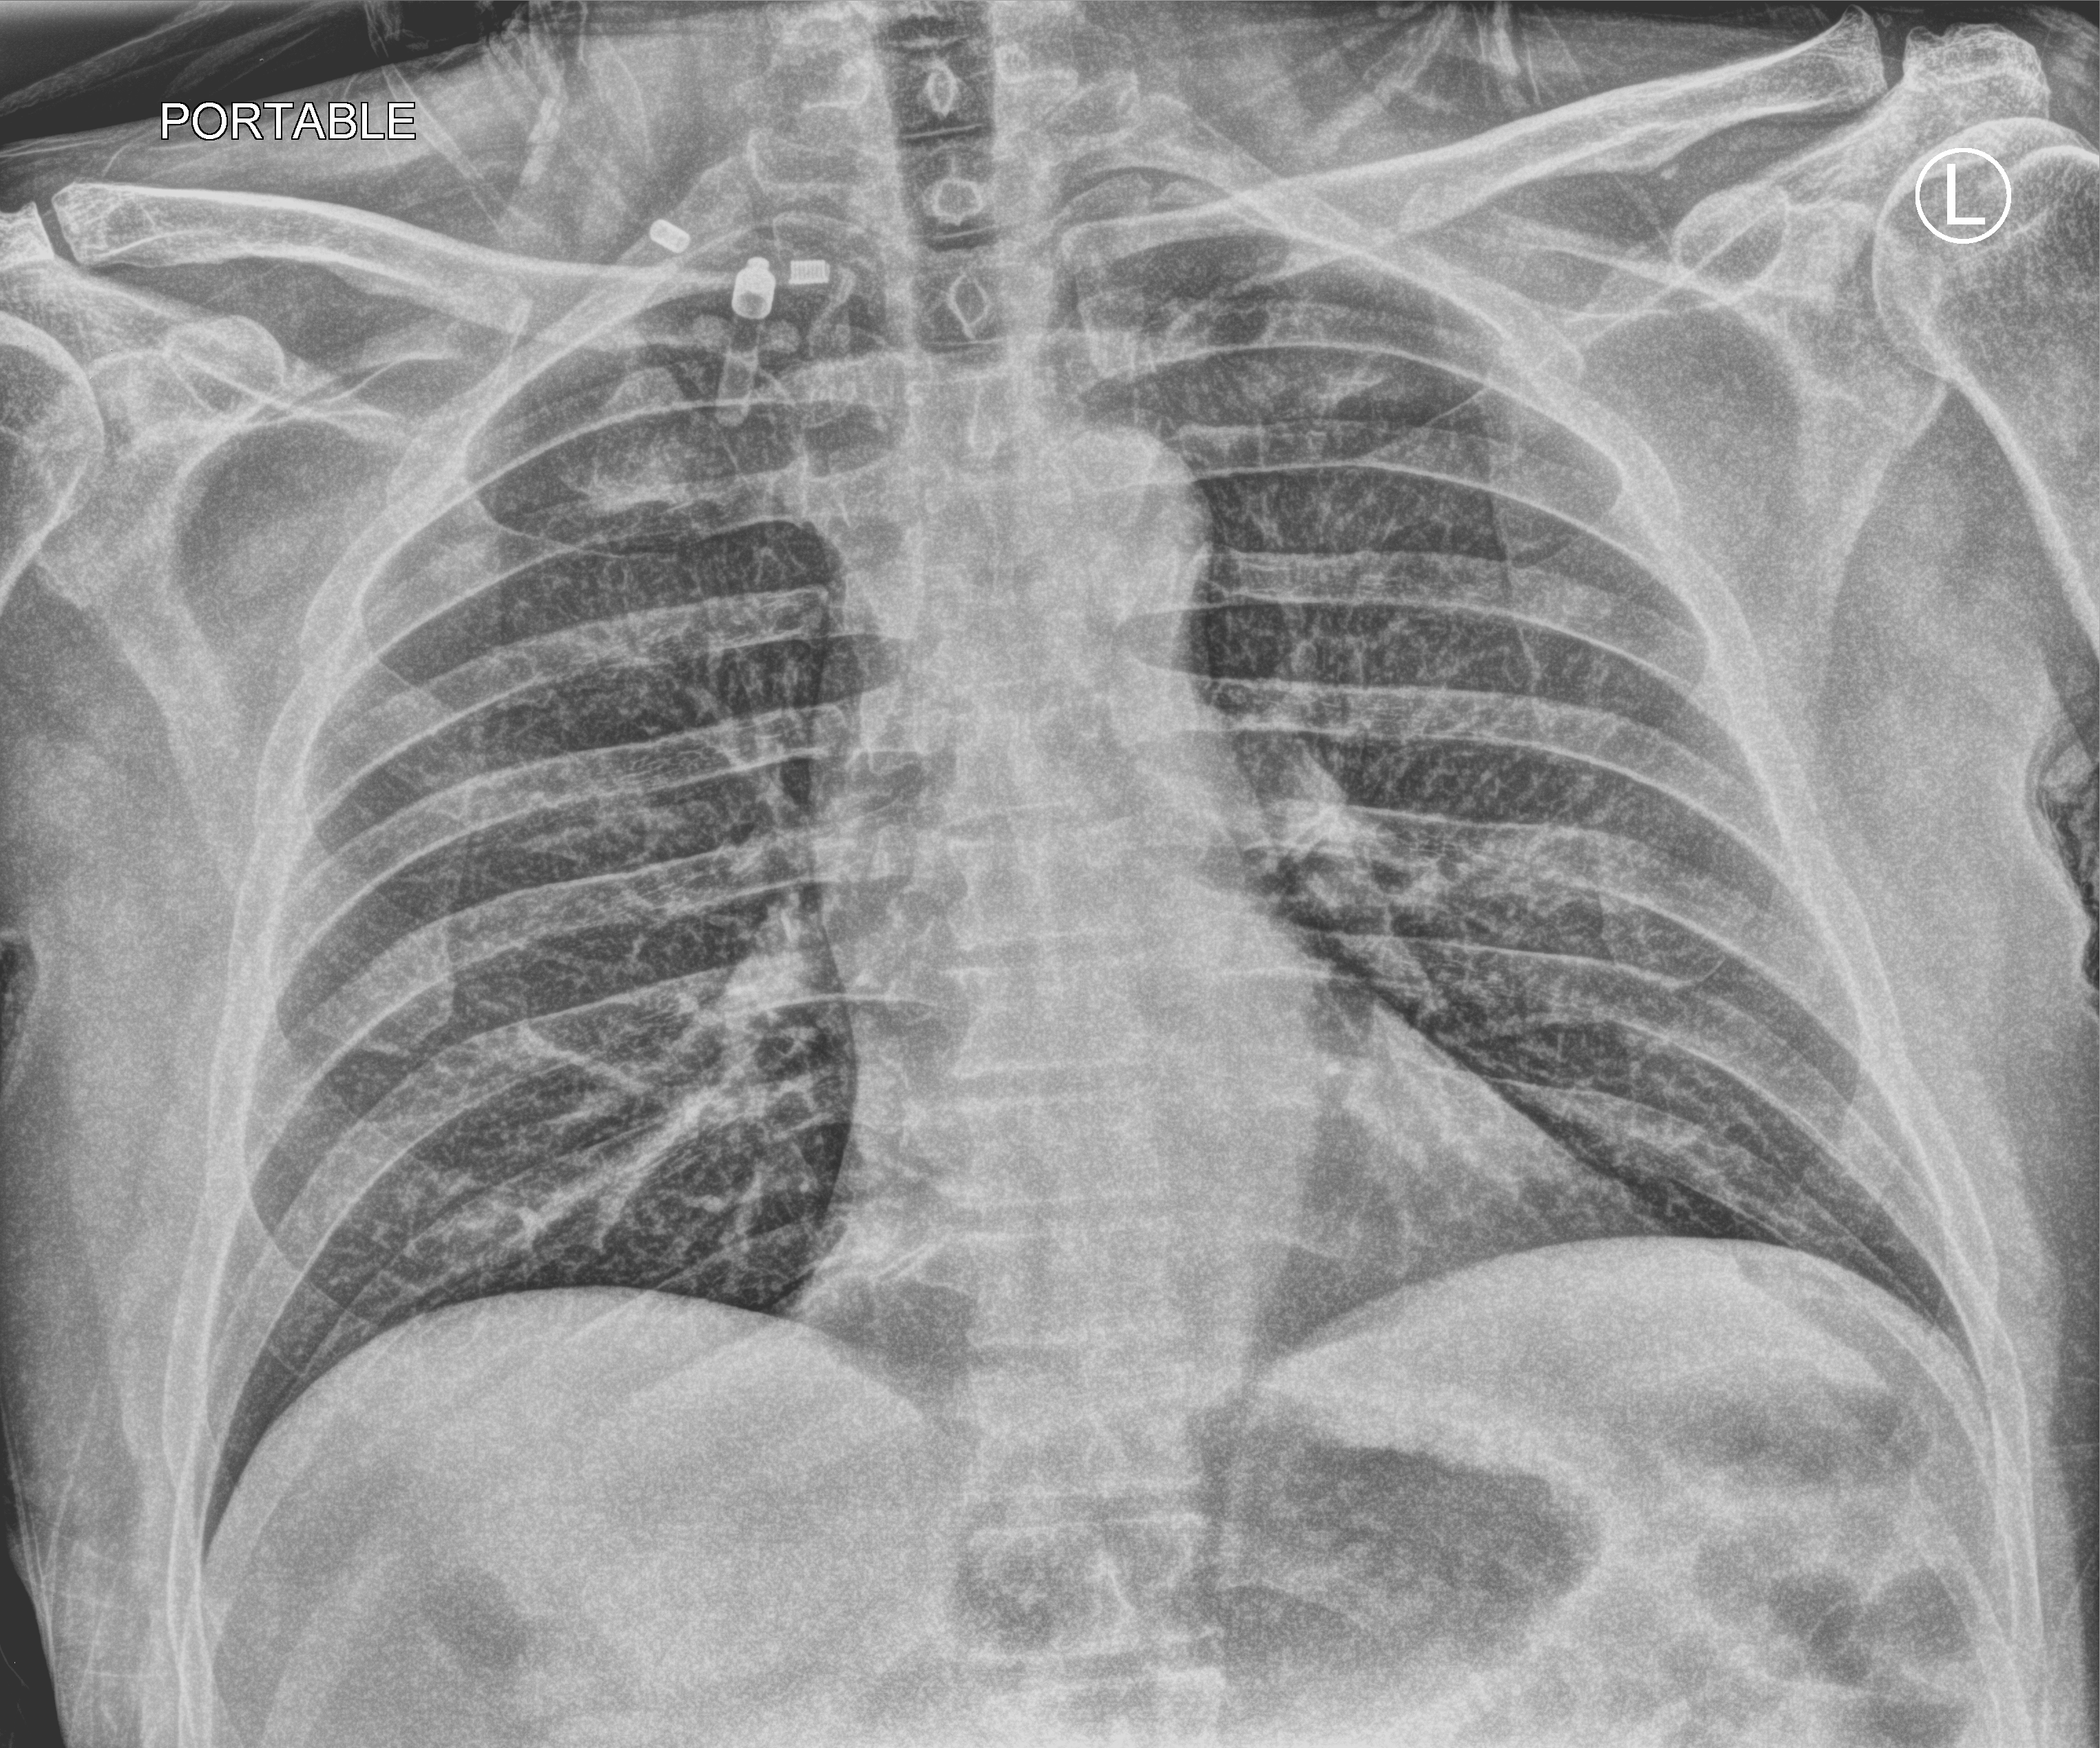
Portable chest radiograph; anteroposterior (AP) projection. Male patient hospitalised with COVID-19, age 60–74 years.
Hospital-stay facts (about this admission, not read from this image; timing relative to this image not recorded): mechanically ventilated during this hospital stay: no; admitted to intensive care during this hospital stay: no.